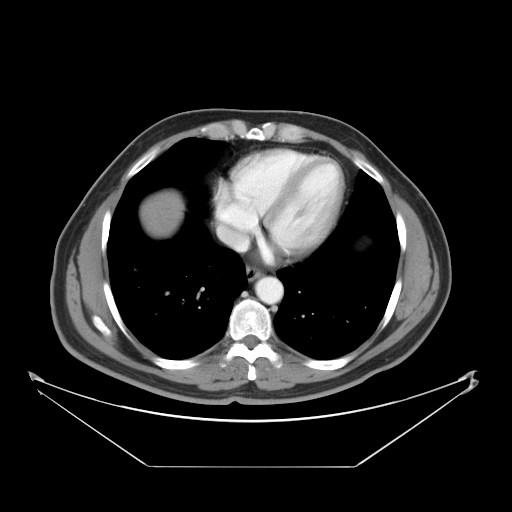
Contrast-enhanced abdominal CT, one axial slice; position 43 of 46 along the scan axis; reconstruction kernel STANDARD; 120 kVp; intravenous contrast given; soft-tissue window (W 400 / L 40 HU); 5 mm slice thickness; 512 × 512 image matrix, field of view 465 × 465 mm. Male patient, age 57 years. From the clinical record (not read from this slice): diagnosis: colorectal cancer liver metastases, imaged before liver resection.
Annotated regions visible in this slice (expert manual segmentation):
- liver: bounding box (x1, y1, x2, y2) in pixels: (142, 194, 181, 236)
- planned liver remnant (the part of the liver to remain after resection): (141, 194, 181, 236)